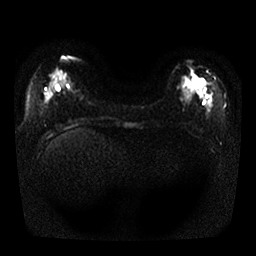
Breast MRI, one axial slice; position 10 of 25 along the scan axis; diffusion-weighted series; image 2 of 4 stored at this slice position (different b-values; order by instance number); 1.5 T; 4 mm slice thickness; 256 × 256 image matrix, field of view 330 × 330 mm. Female patient.
Structures marked on this image (expert manual segmentation):
- tumour on diffusion-weighted imaging: bounding box [x1, y1, x2, y2] px = [183, 76, 205, 91]